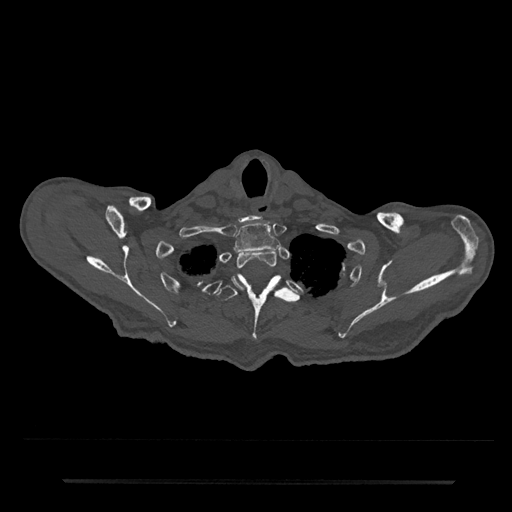
CT including the spine, one axial slice. Slice 685 of 797 in the series (ordered by position). 120 kVp. Bone window (W 1800 / L 400 HU). 512 × 512 image matrix, field of view 427 × 427 mm. Patient: male, 74 years. From the clinical record (not read from this slice): primary cancer: prostate.
Annotated regions visible in this slice (semi-automatic segmentation, software-assisted and operator-edited):
- T1 vertebra: bounding box (x1, y1, x2, y2) in pixels: (233, 222, 281, 253)
- T2 vertebra: (232, 250, 277, 289)
- T3 vertebra: (216, 274, 299, 342)